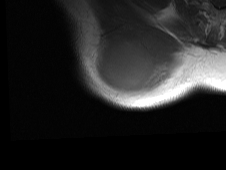
MRI of an extremity soft-tissue mass, one axial slice; position 57 of 81 along the scan axis; MR volume resampled by the dataset authors to the PET/CT grid (not the native acquisition matrix); 3.27 mm slice thickness; 226 × 170 image matrix. Male patient. From the clinical record (not read from this slice): histological type: pleiomorphic spindle cell undifferentiated; grade: high; site of the primary tumour: right parascapusular.
Structures marked on this image (expert contour drawn on MRI and transferred to this co-registered scan by the dataset authors):
- gross tumour volume including surrounding oedema: bounding box <94,33,191,103> (left, top, right, bottom; pixels)
- gross tumour volume (mass): <97,40,163,100>